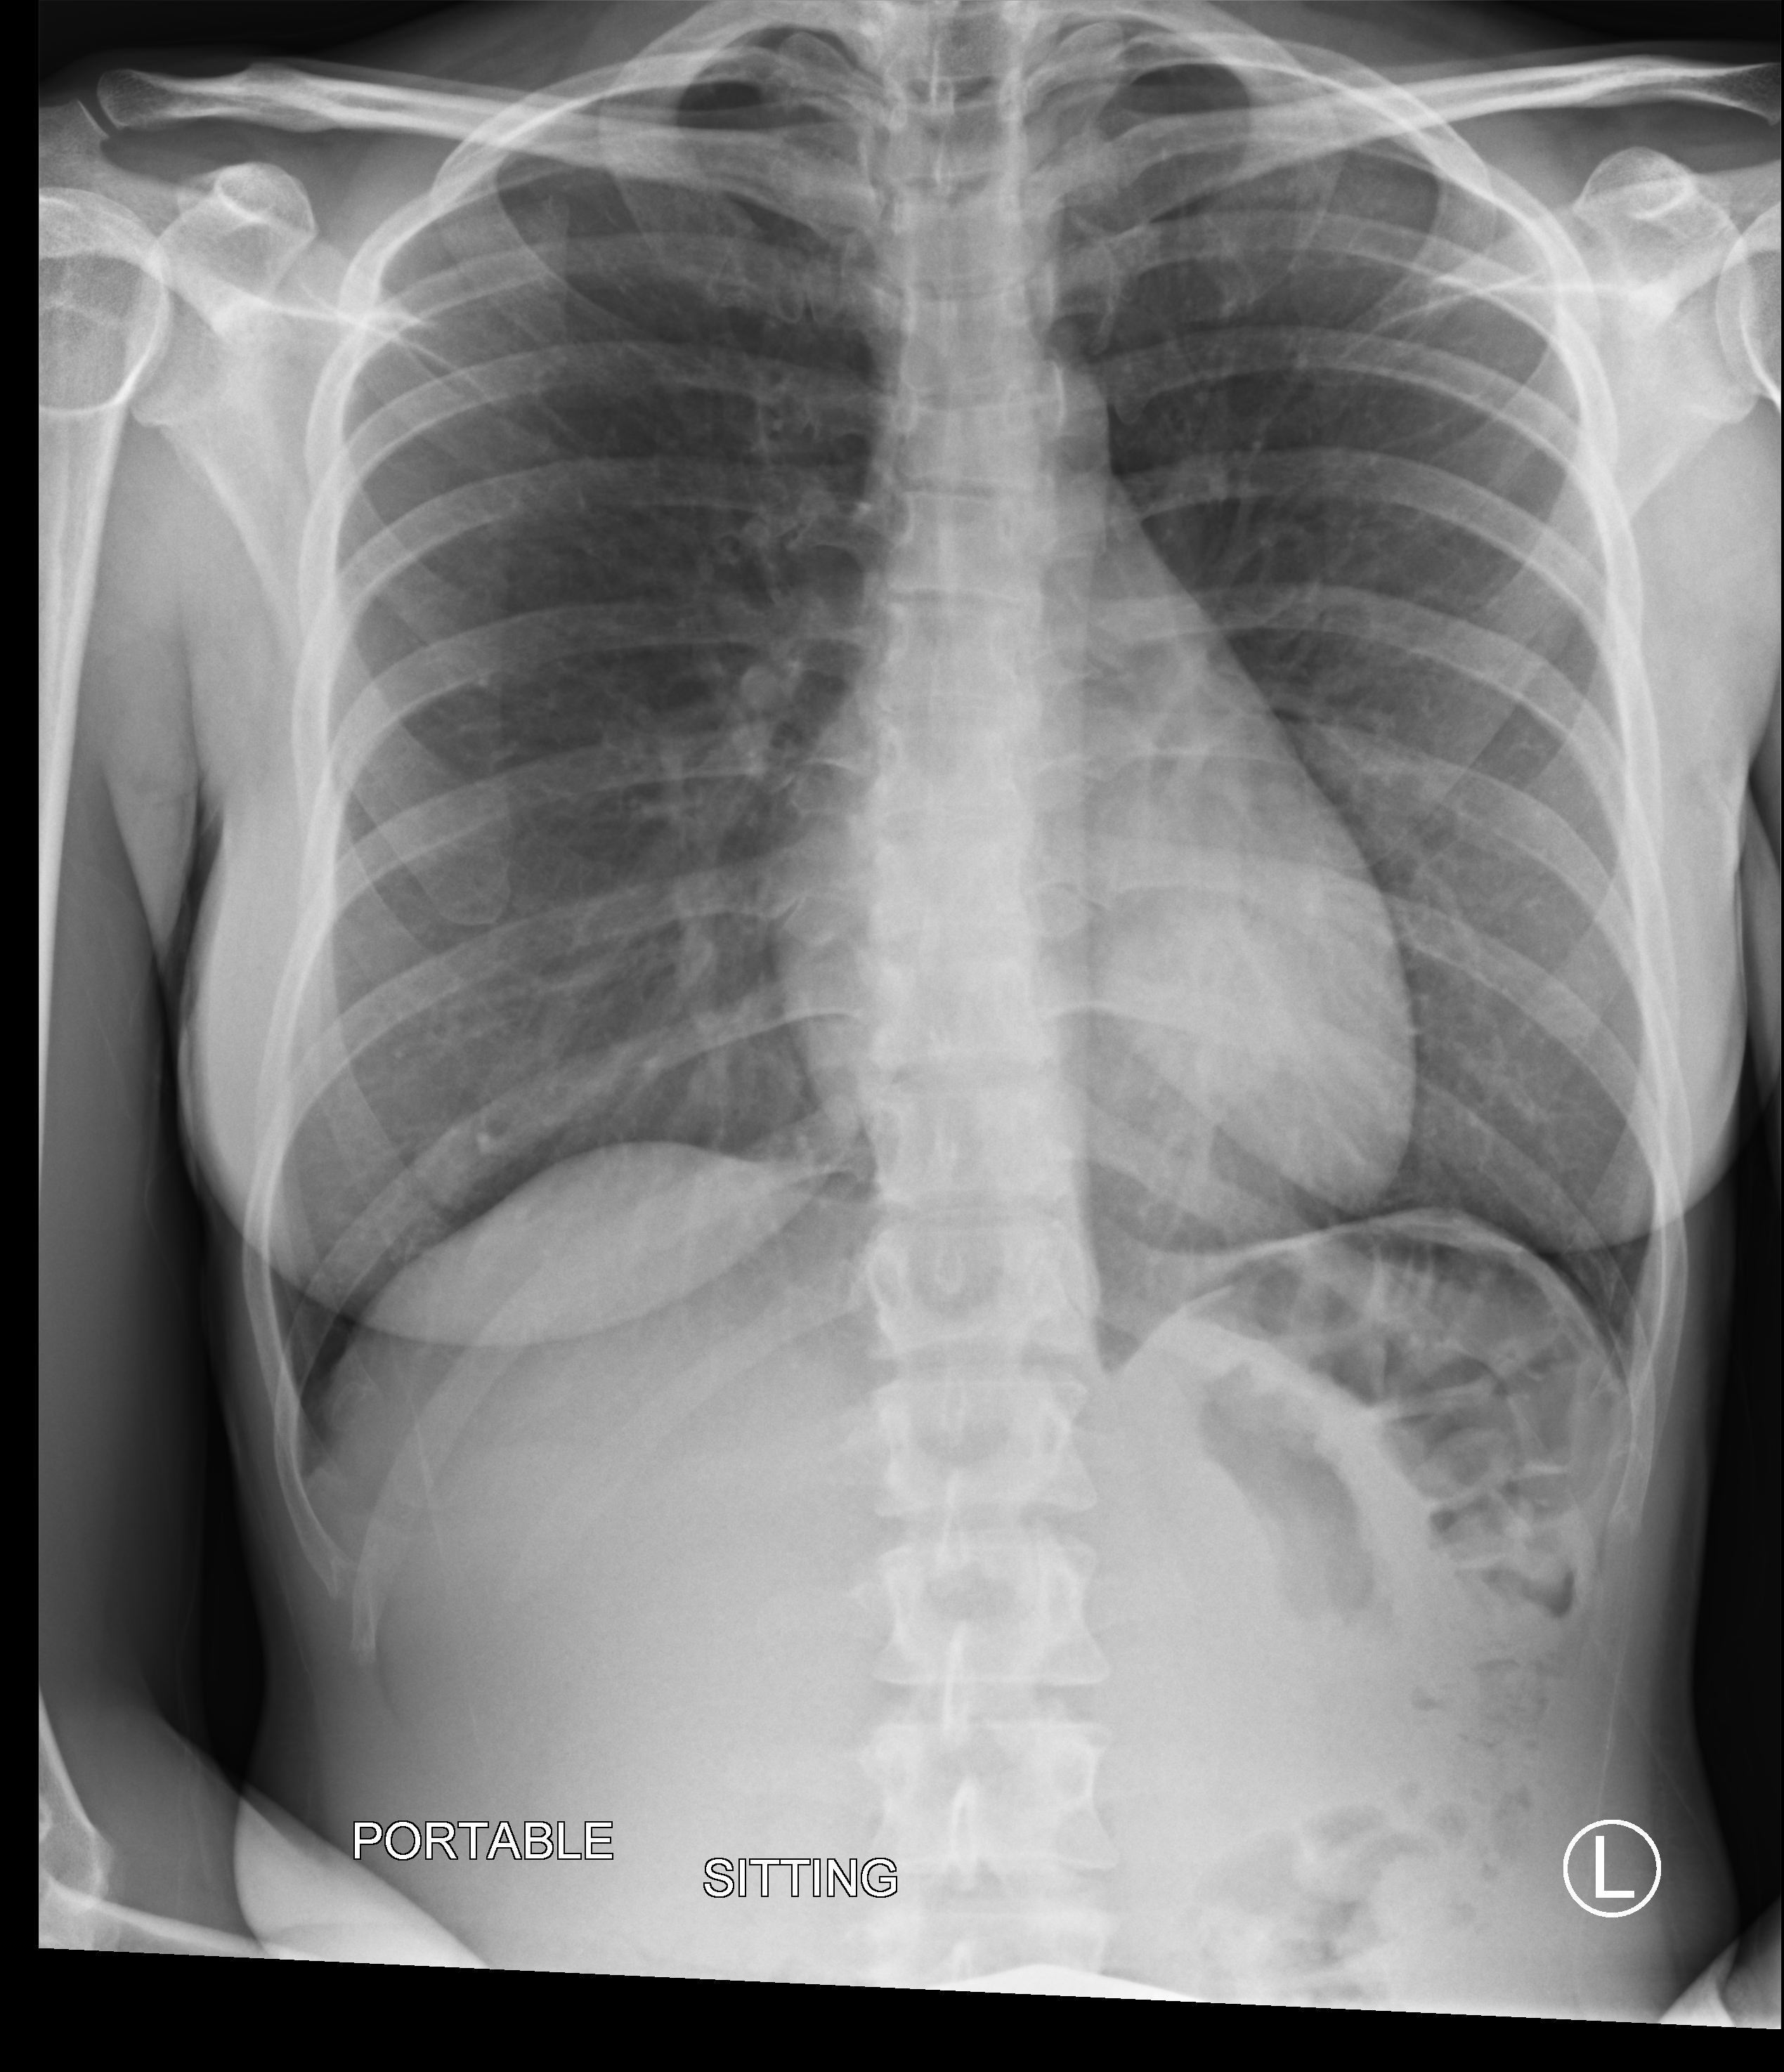
Chest X-ray (portable); anteroposterior (AP) projection. Female patient hospitalised with COVID-19, age 18–59 years.
Hospital-stay facts (about this admission, not read from this image; timing relative to this image not recorded): mechanically ventilated during this hospital stay: no; admitted to intensive care during this hospital stay: no; chronic kidney disease (admission record): no.